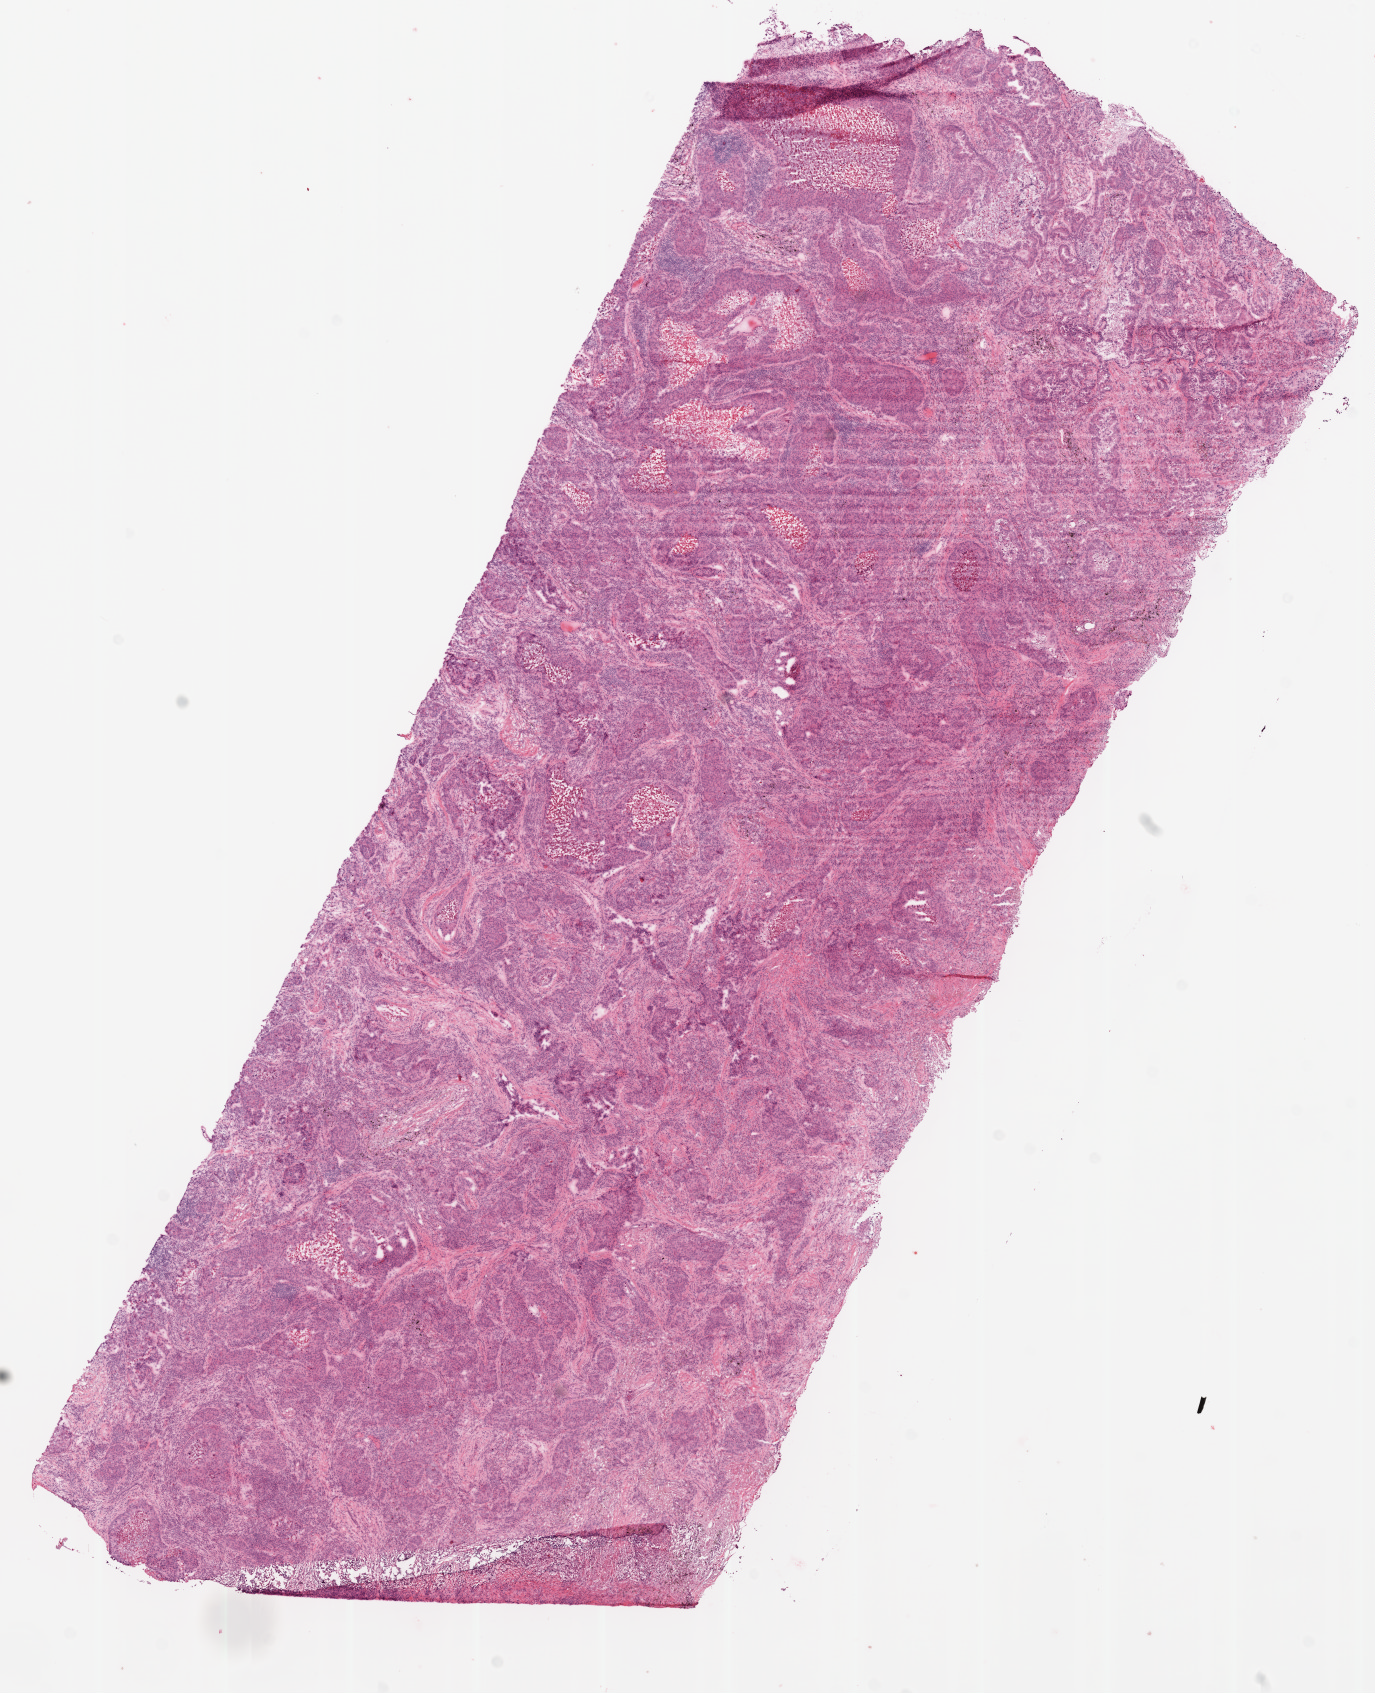
Digitized H&E-stained tissue section (whole slide), low-resolution overview of the scanned area, about 11.0 x 13.6 mm. Frozen section. Lung, primary tumour sample. Female, age 60 years at initial diagnosis. Composition of this section per pathologist review: tumour cells 65%, tumour nuclei 70%, normal cells 0%, stromal cells 20%, necrosis 15%.
Histologic diagnosis: Squamous cell carcinoma, NOS (upper lobe, lung). AJCC pathologic stage: IIIA. TNM: T3 N2 M0.